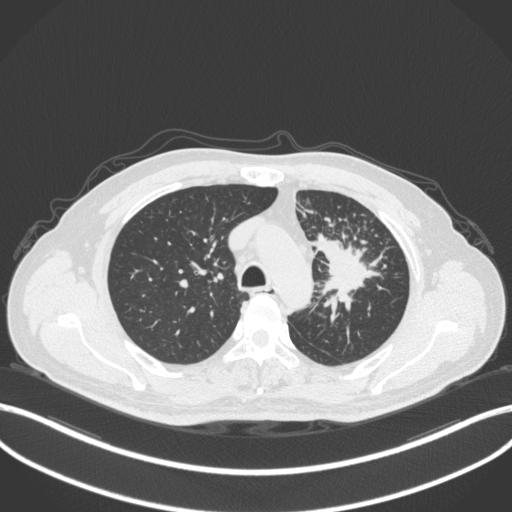
Chest CT, one axial slice; slice 264 of 386 in the series (ordered by position); reconstruction kernel B31f; lung window (W 1500 / L -600 HU); 512 × 512 image matrix, field of view 400 × 400 mm. Patient: male, 69 years. From the clinical record (not read from this slice): clinical TNM (as recorded): T2a N2 M0.
Outlined on this slice (rectangle marked by the reading radiologist):
- lung tumour (recorded histology: adenocarcinoma): bounding box (x1, y1, x2, y2) in pixels: (312, 229, 380, 306)